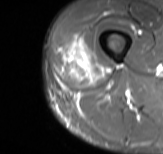
MRI of an extremity soft-tissue mass, one axial slice; position 20 of 61 along the scan axis; STIR; MR volume resampled by the dataset authors to the PET/CT grid (not the native acquisition matrix); 3.27 mm slice thickness; 163 × 154 image matrix, field of view 159 × 150 mm. Male patient. From the clinical record (not read from this slice): histological type: poorly differentiated synovial sarcoma; grade: high; site of the primary tumour: right buttock.
Outlined on this slice (expert contour drawn on MRI and transferred to this co-registered scan by the dataset authors):
- gross tumour volume including surrounding oedema: bounding box <59,37,106,86> (left, top, right, bottom; pixels)